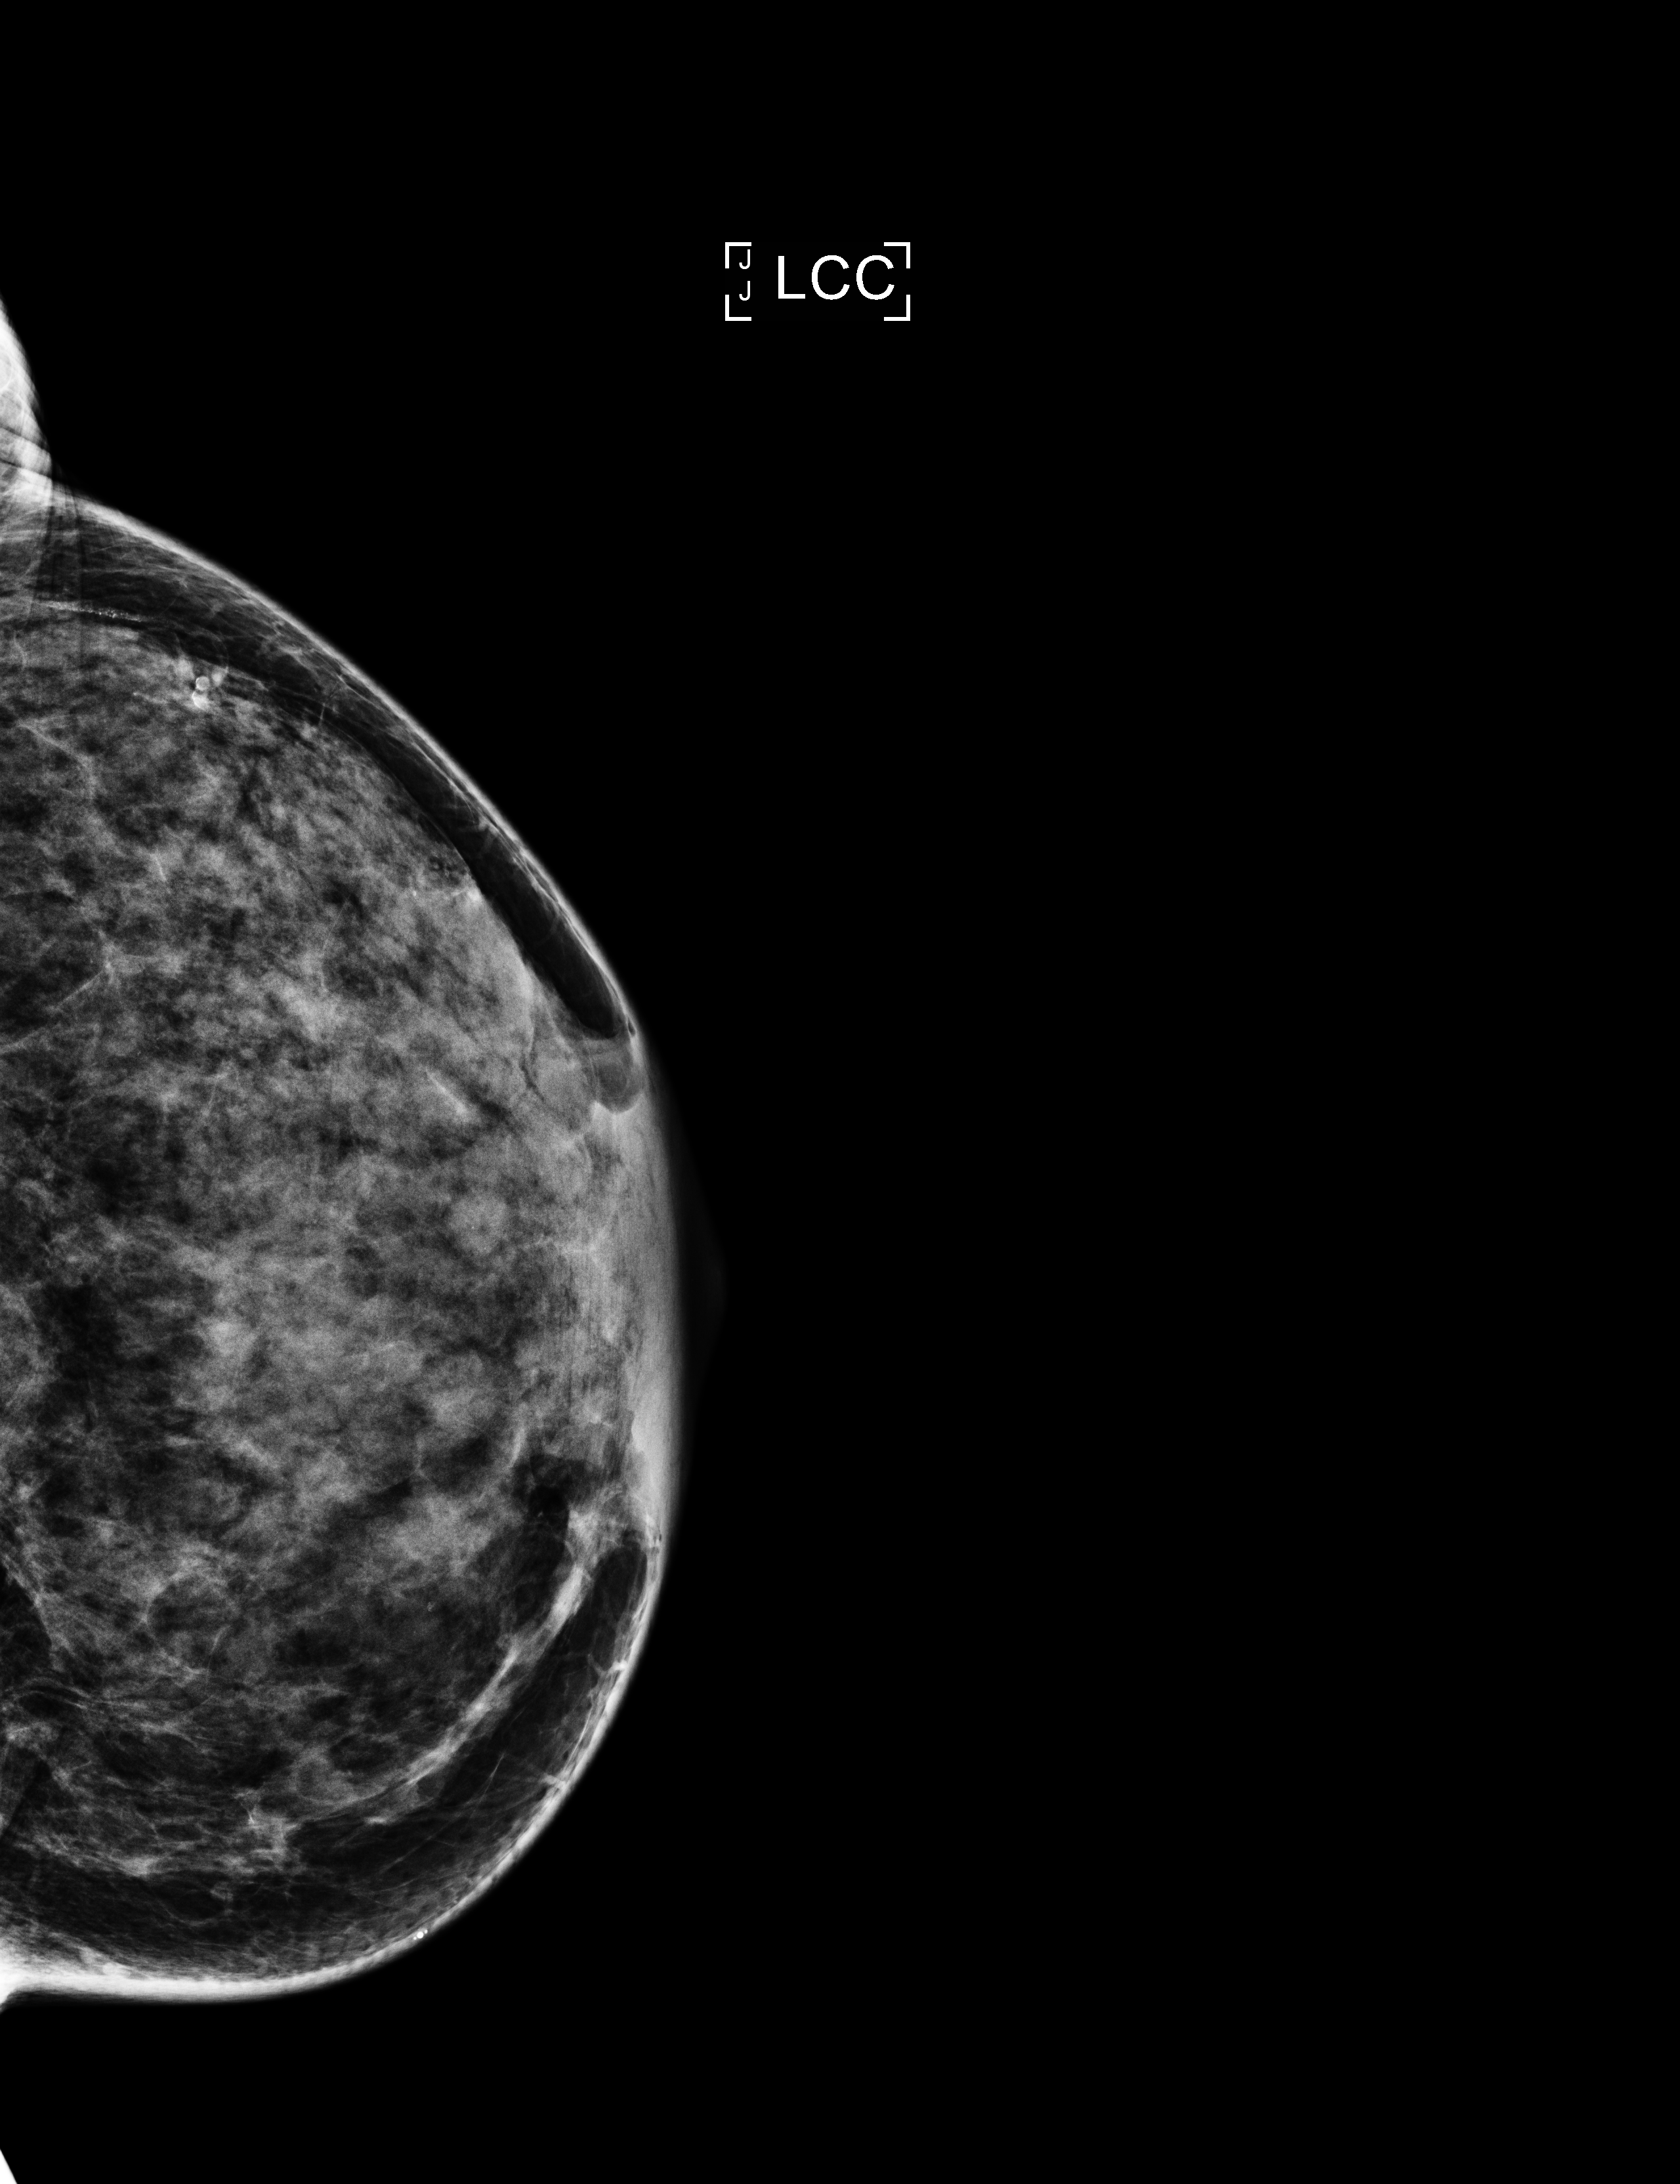
Digital mammogram (FFDM); left breast; cranio-caudal projection; screening examination; compressed breast thickness 46 mm; system: Selenia Dimensions. Patient aged 56 years (female).
Breast density at the screening exam (both breasts): almost entirely fatty (BI-RADS density category a). Final BI-RADS assessment for this screening round (tomosynthesis exam, both breasts): category 1. Recall: no recall after this screen.